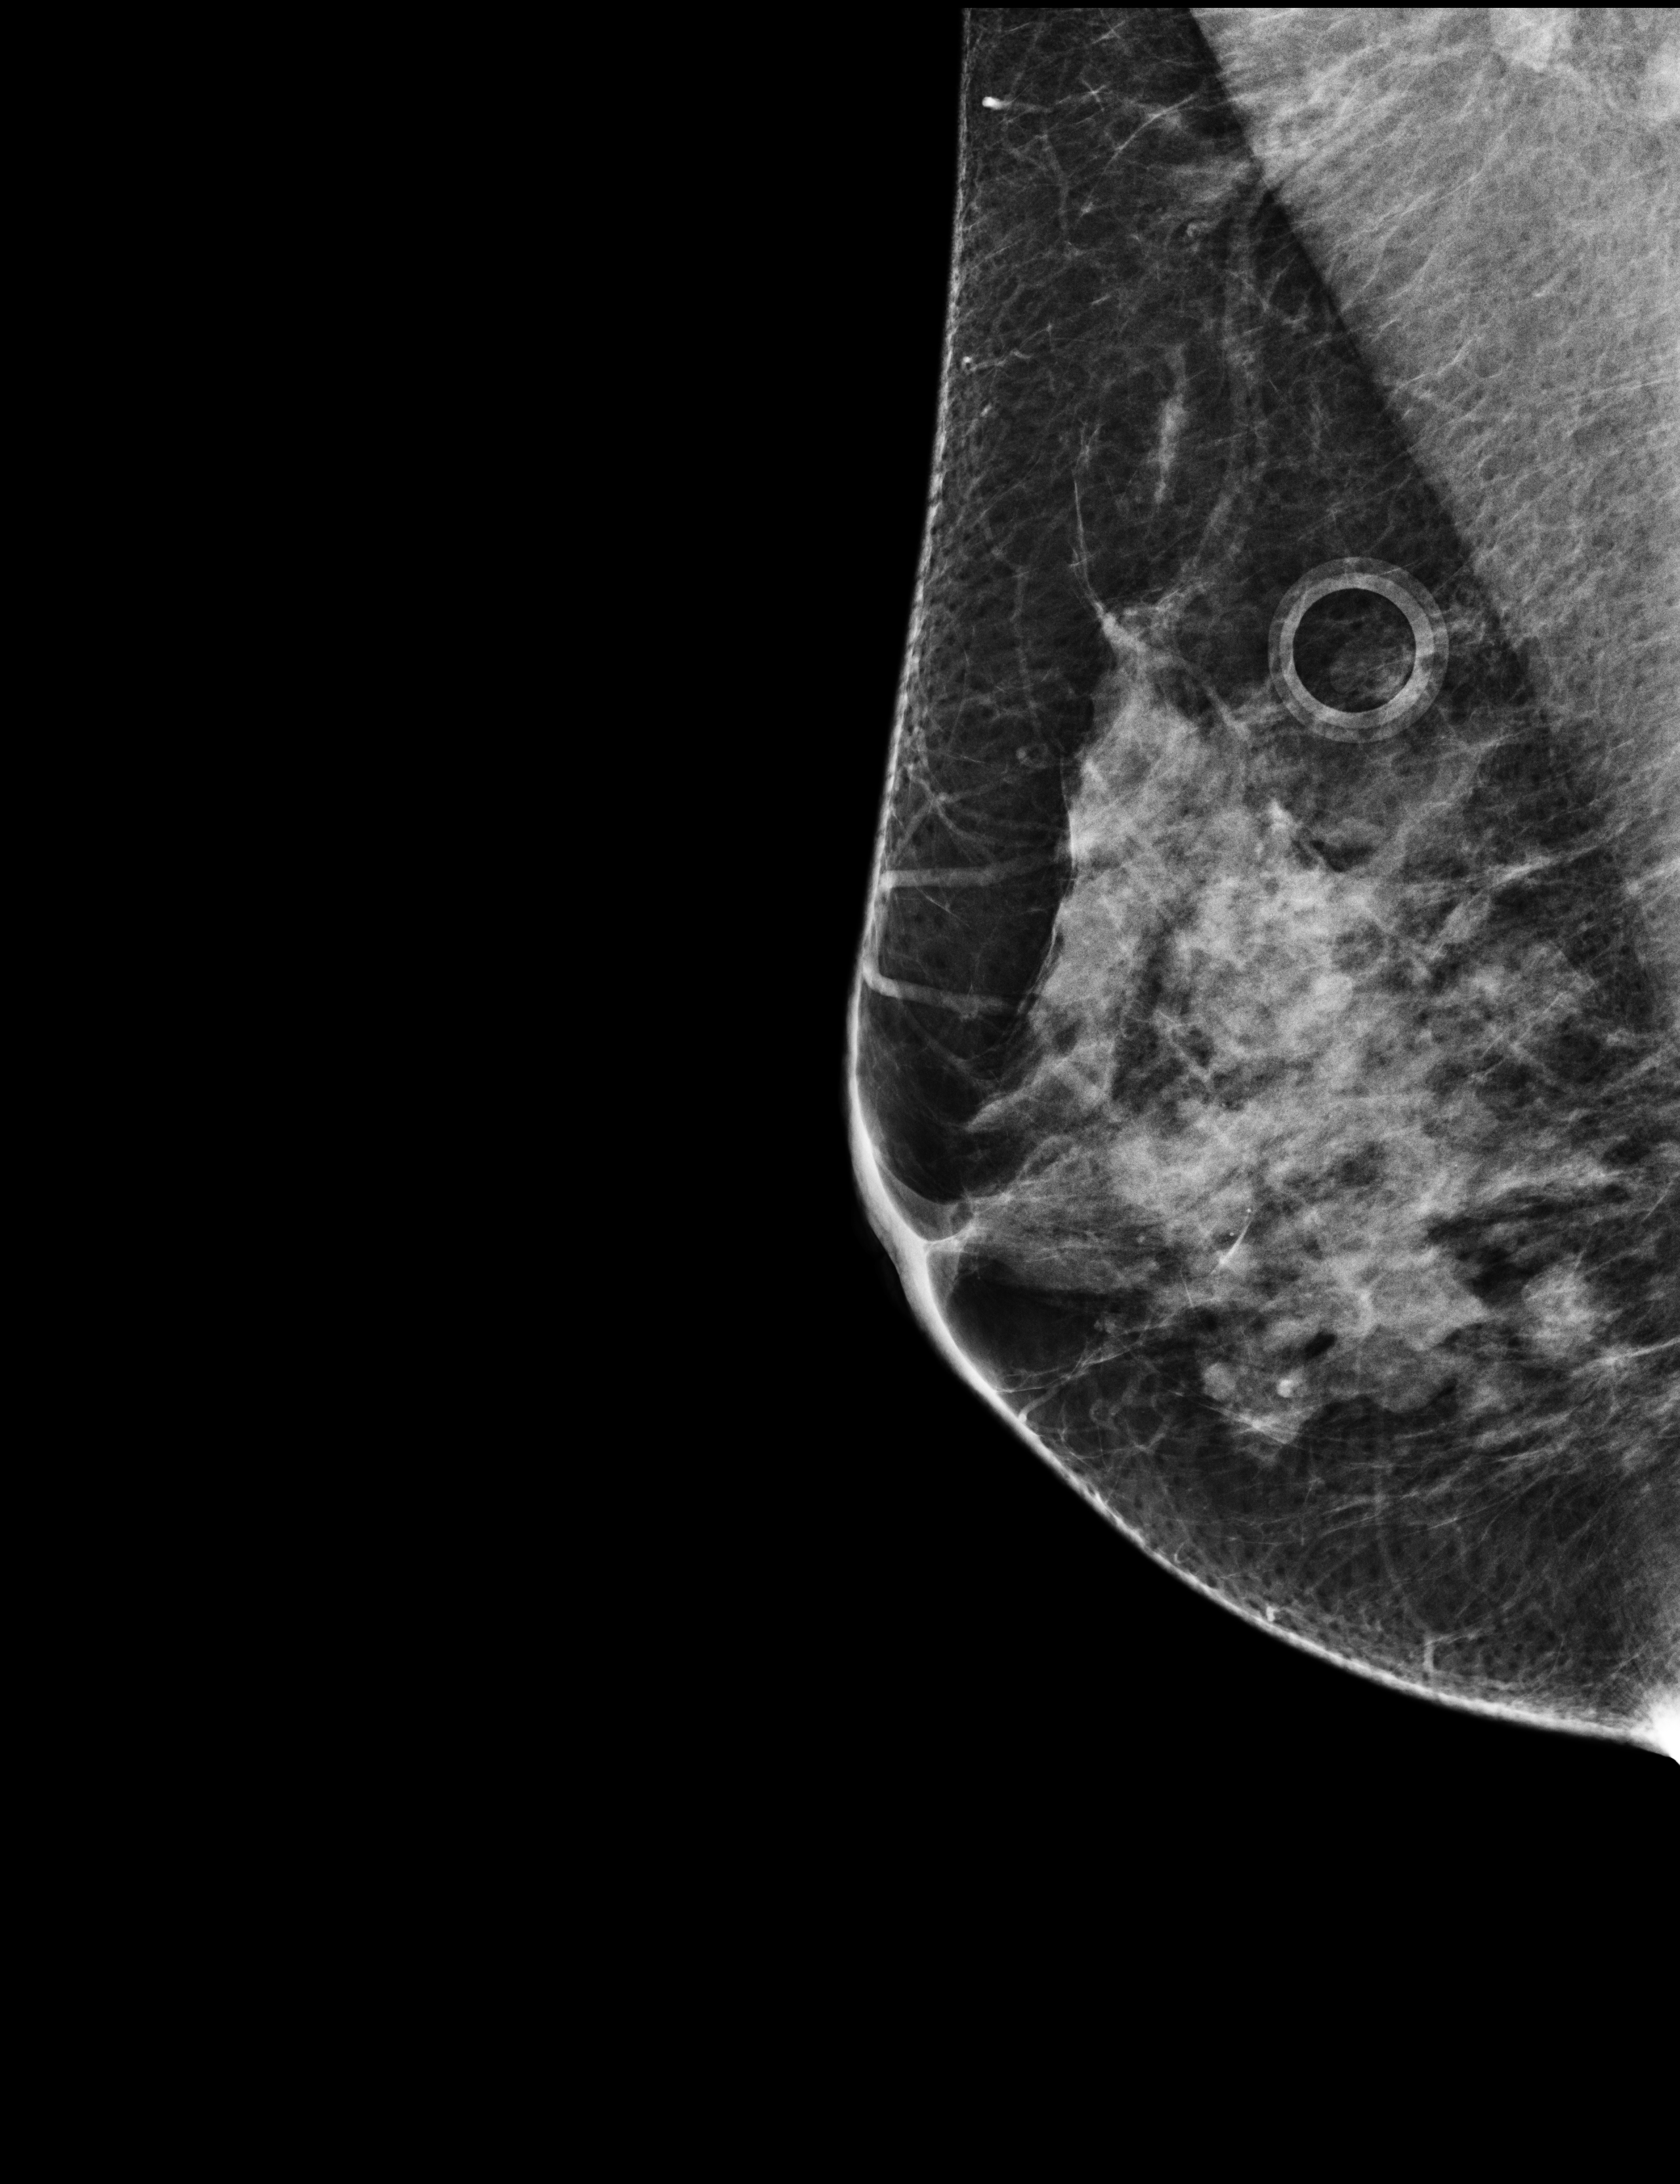
Digital mammogram (FFDM); right breast; MLO view; screening examination; compressed breast thickness 61 mm. Patient: female, 58 years.
BI-RADS breast density category at the screening exam (both breasts, scale 1–4): 3. Final BI-RADS assessment for this screening round (tomosynthesis exam, both breasts): category 4. Recall: recalled for additional imaging after this screen.